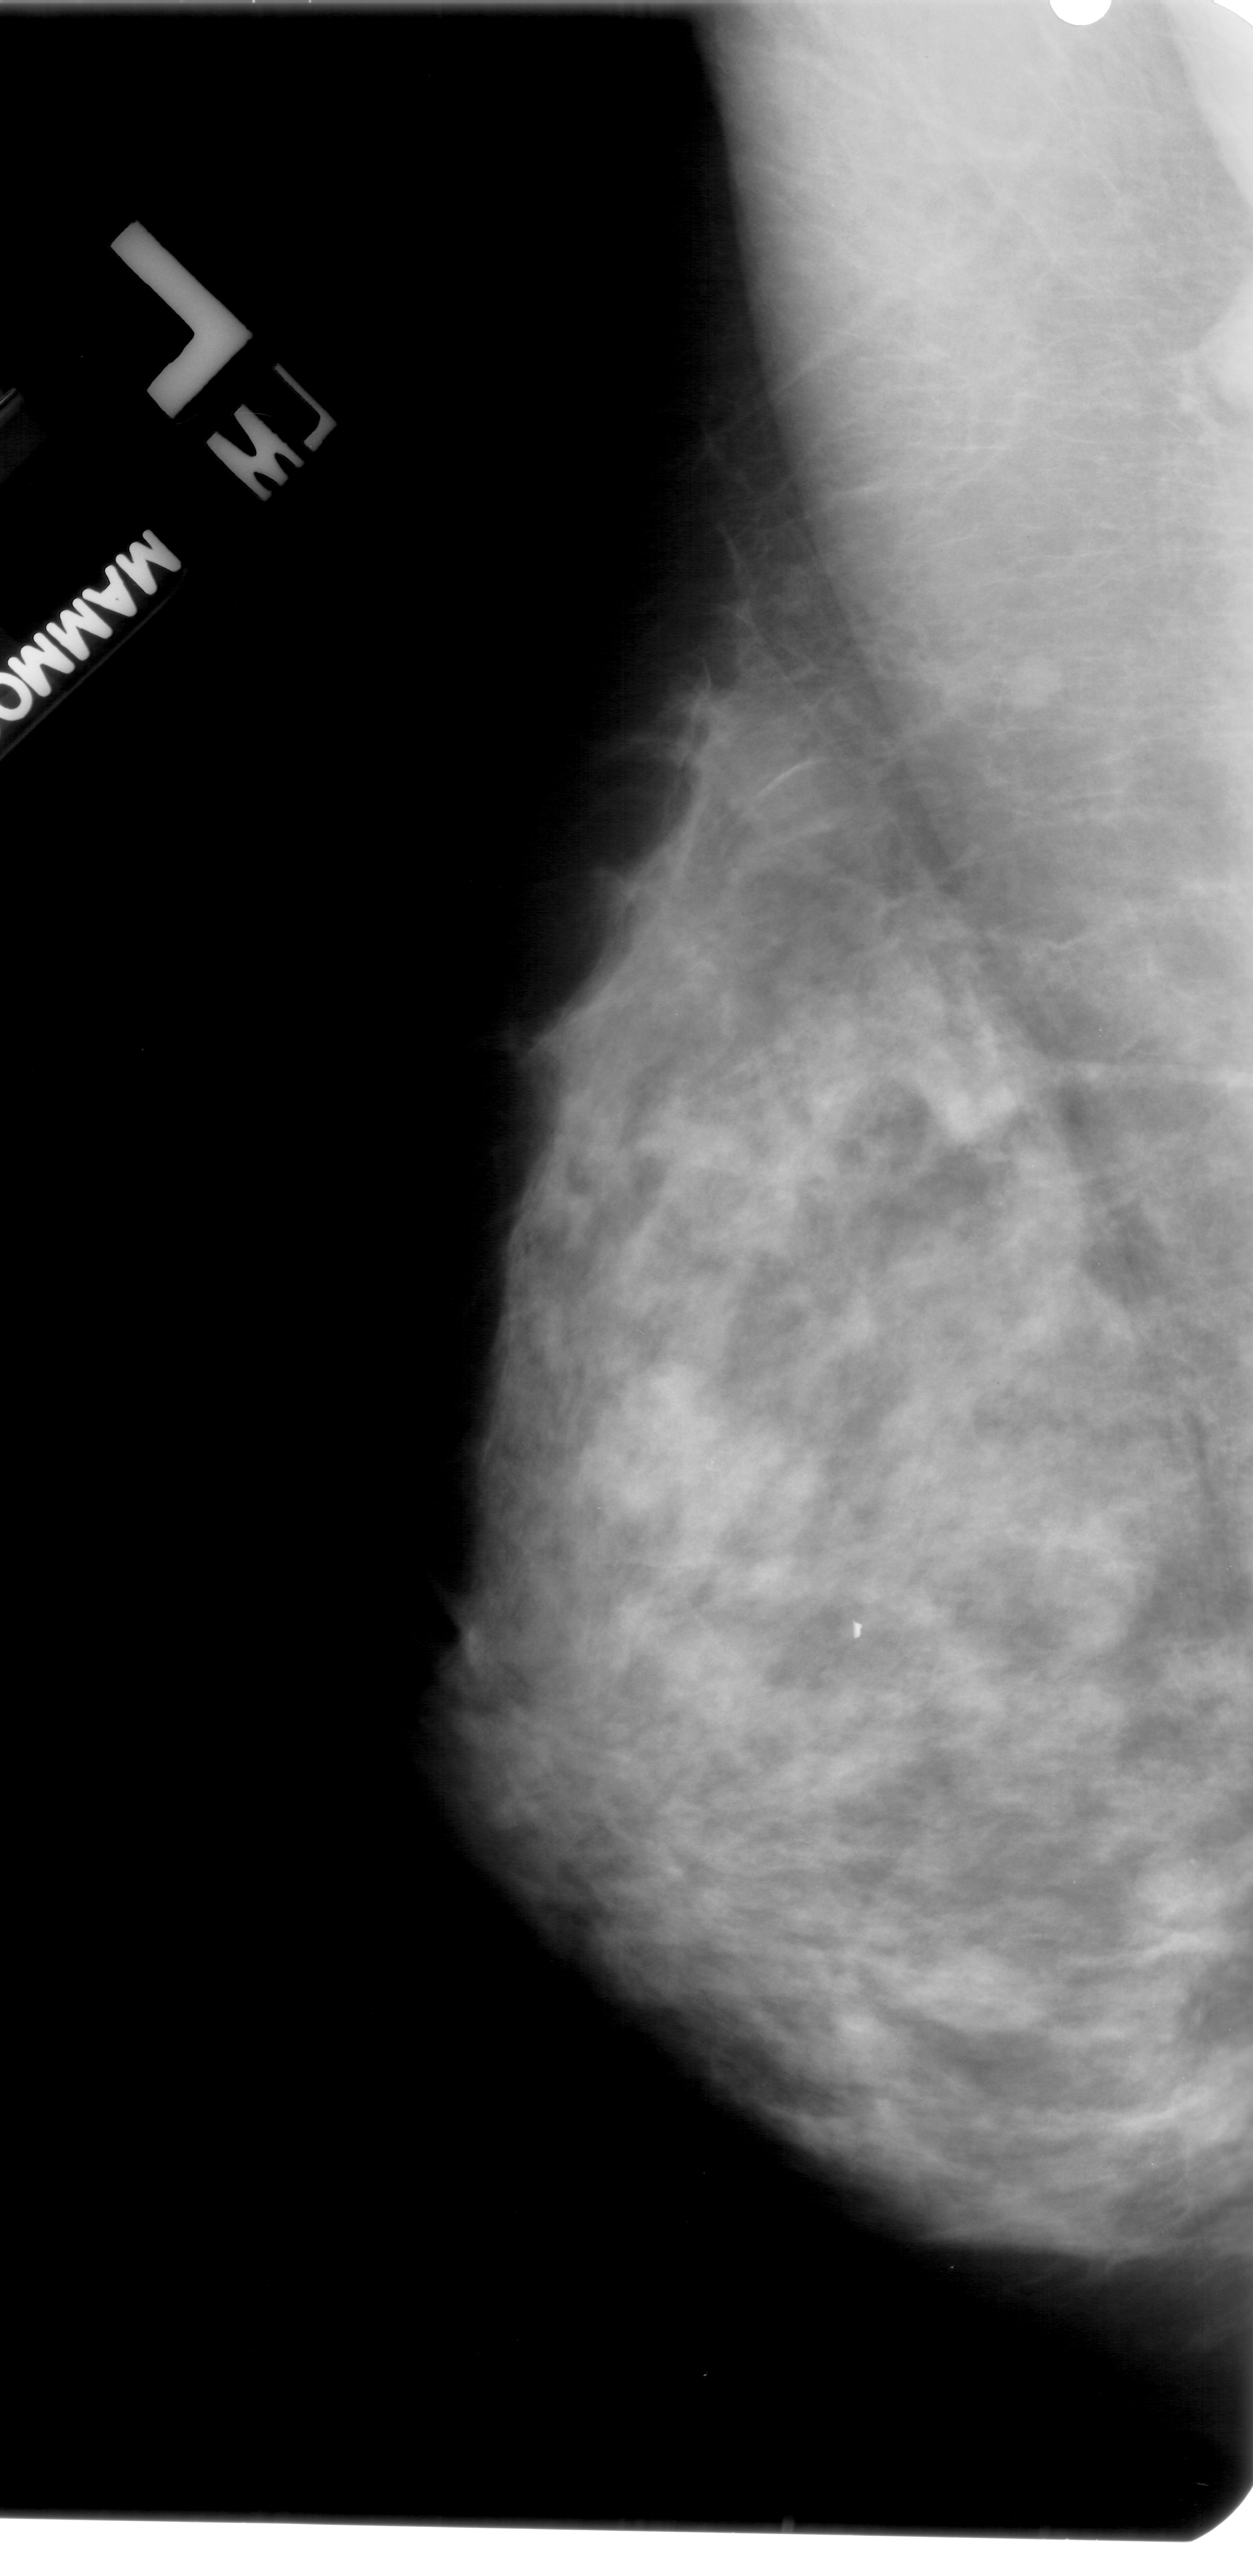
Mammogram (digitized film). Left breast. Mediolateral oblique (MLO) view. BI-RADS breast density category 4 (scale 1–4). 1253 × 2576 image matrix.
Expert-marked regions of interest on this image (one box per marked abnormality):
- calcifications, morphology pleomorphic, distribution clustered; BI-RADS assessment category 4; subtlety rating 1 on a 1 (subtle) to 5 (obvious) scale; pathology (as recorded): benign: box from (x=685, y=1439) to (x=758, y=1497) px